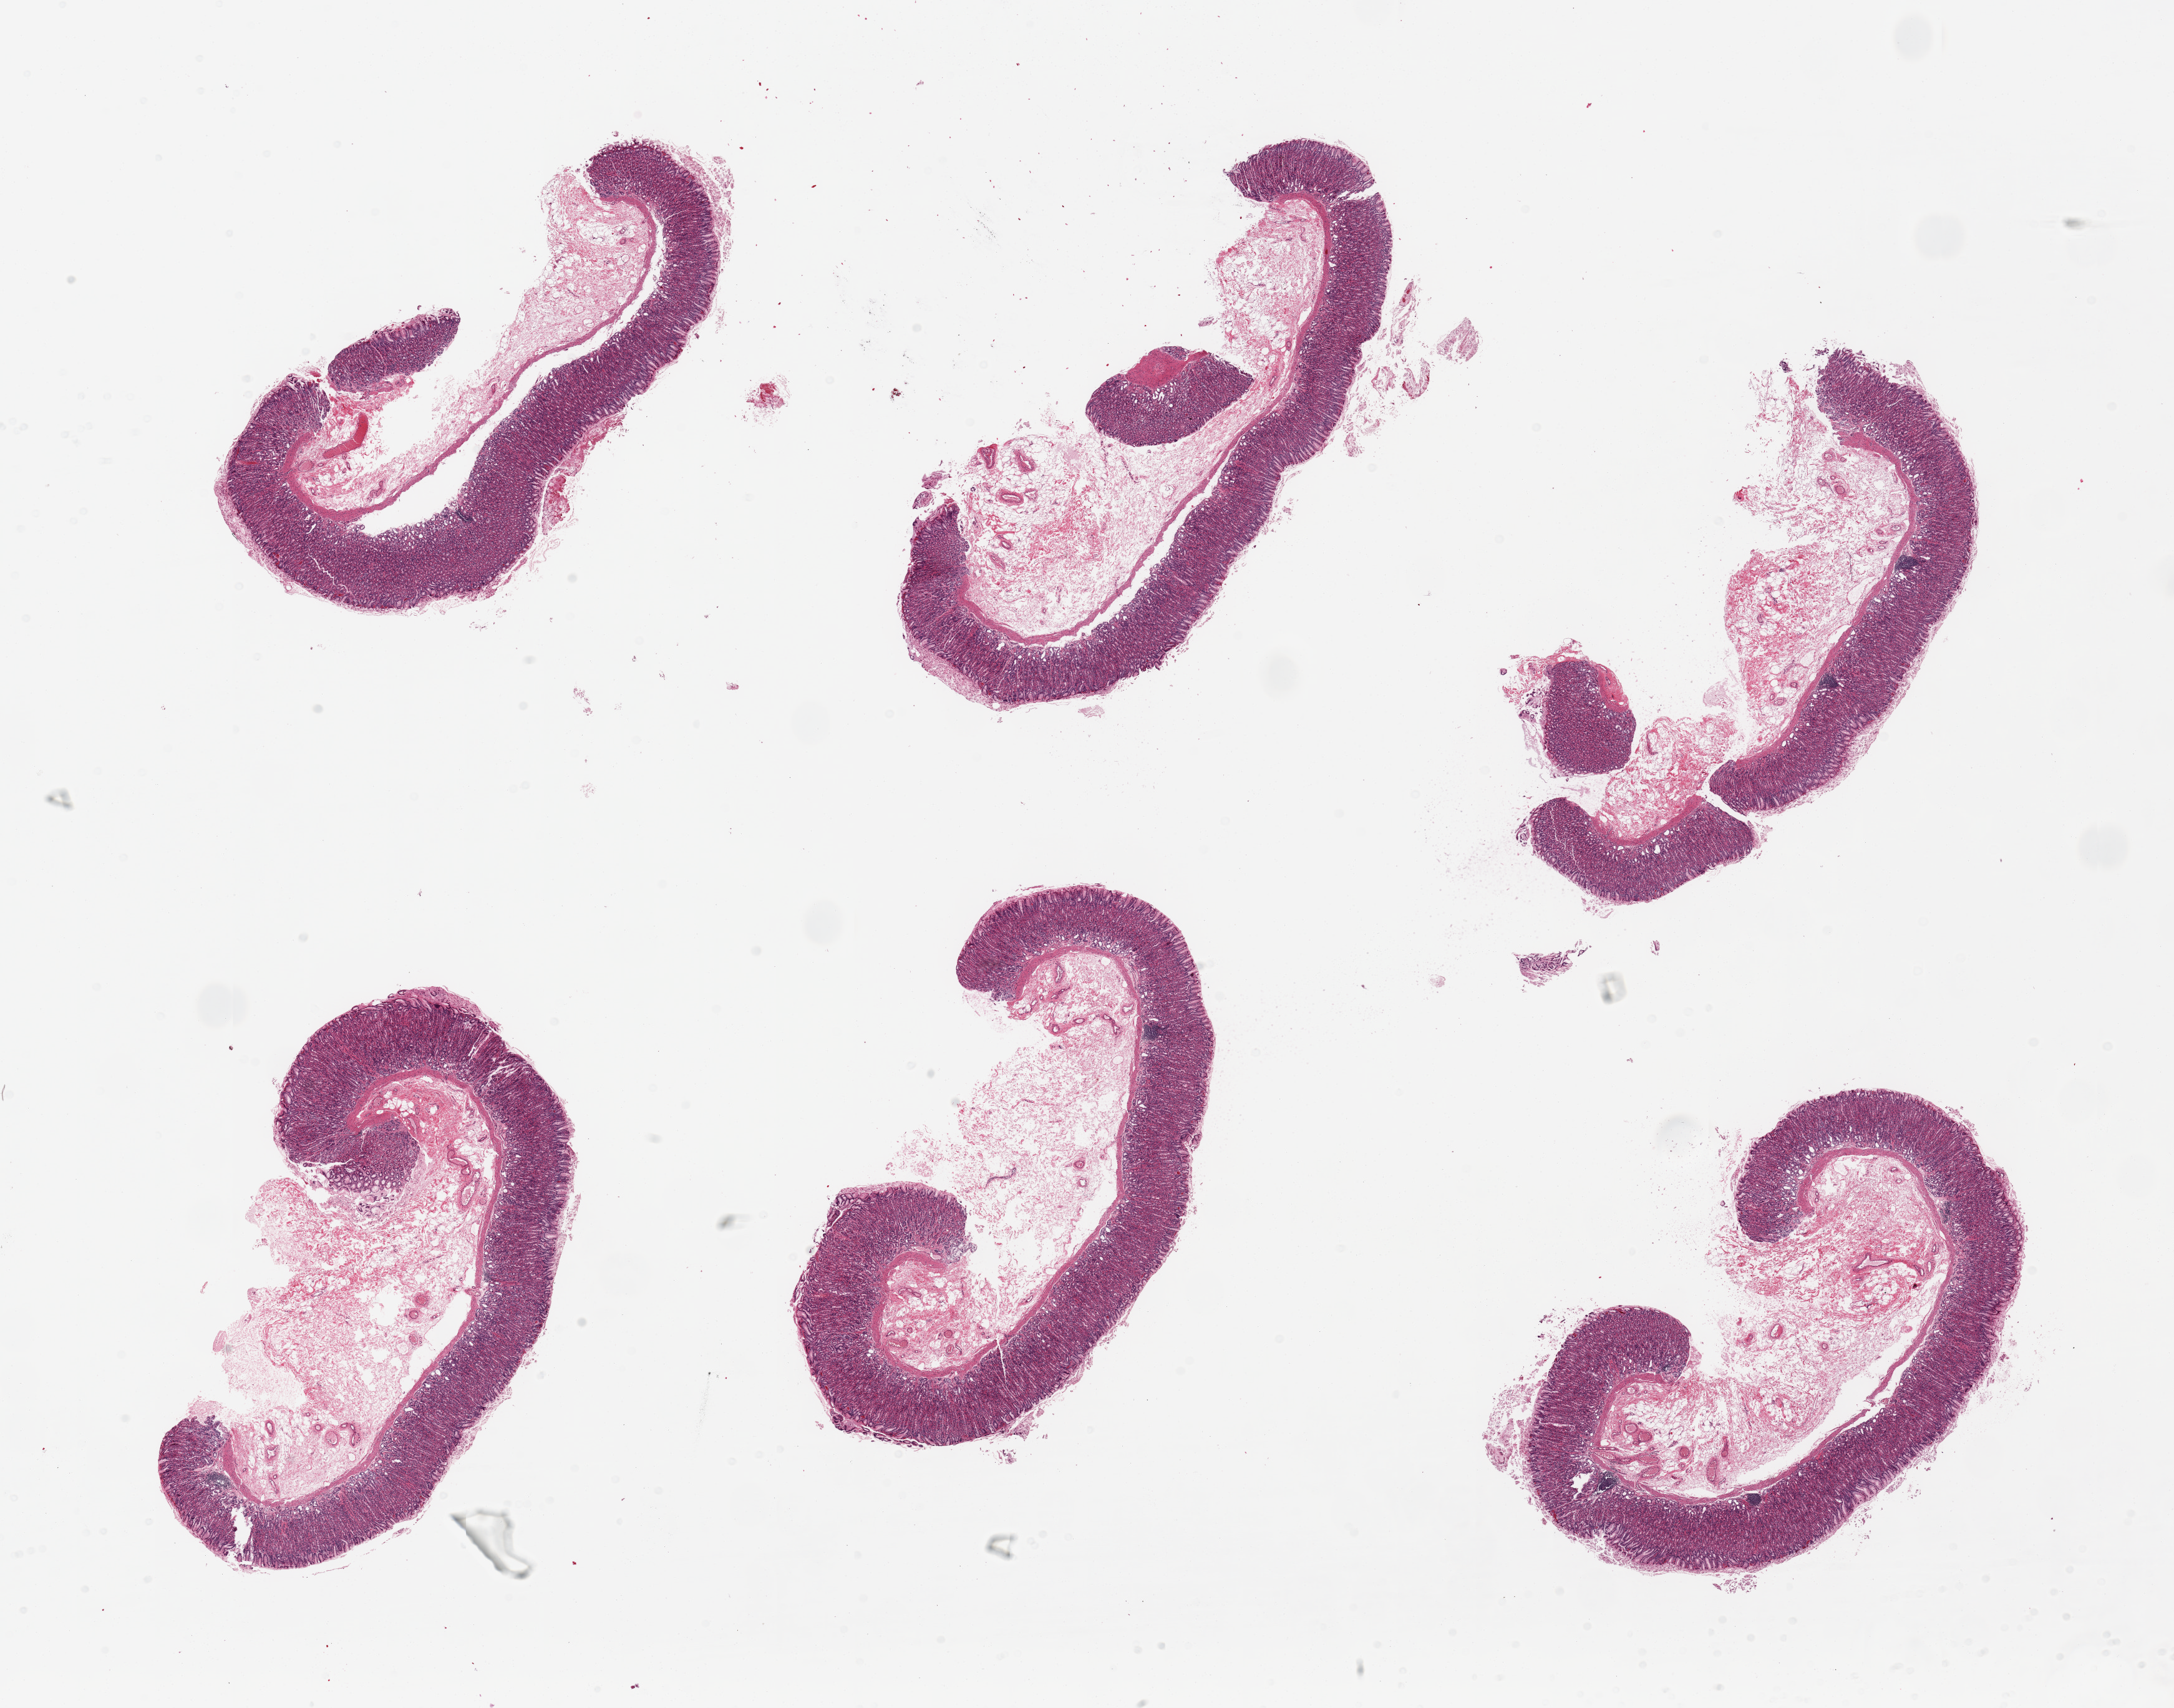
Whole-slide image, hematoxylin and eosin (H&E) stain — low-resolution overview of the scanned area, about 27.6 x 21.7 mm. PAXgene-fixed, paraffin-embedded tissue. Section of stomach (target tissue). Donor tissue sample. Donor sex: female.
Review note (as recorded): 6 pieces, up to 8.5x4mm; mucosa remarkably well-preserved, 20-30% thickness.